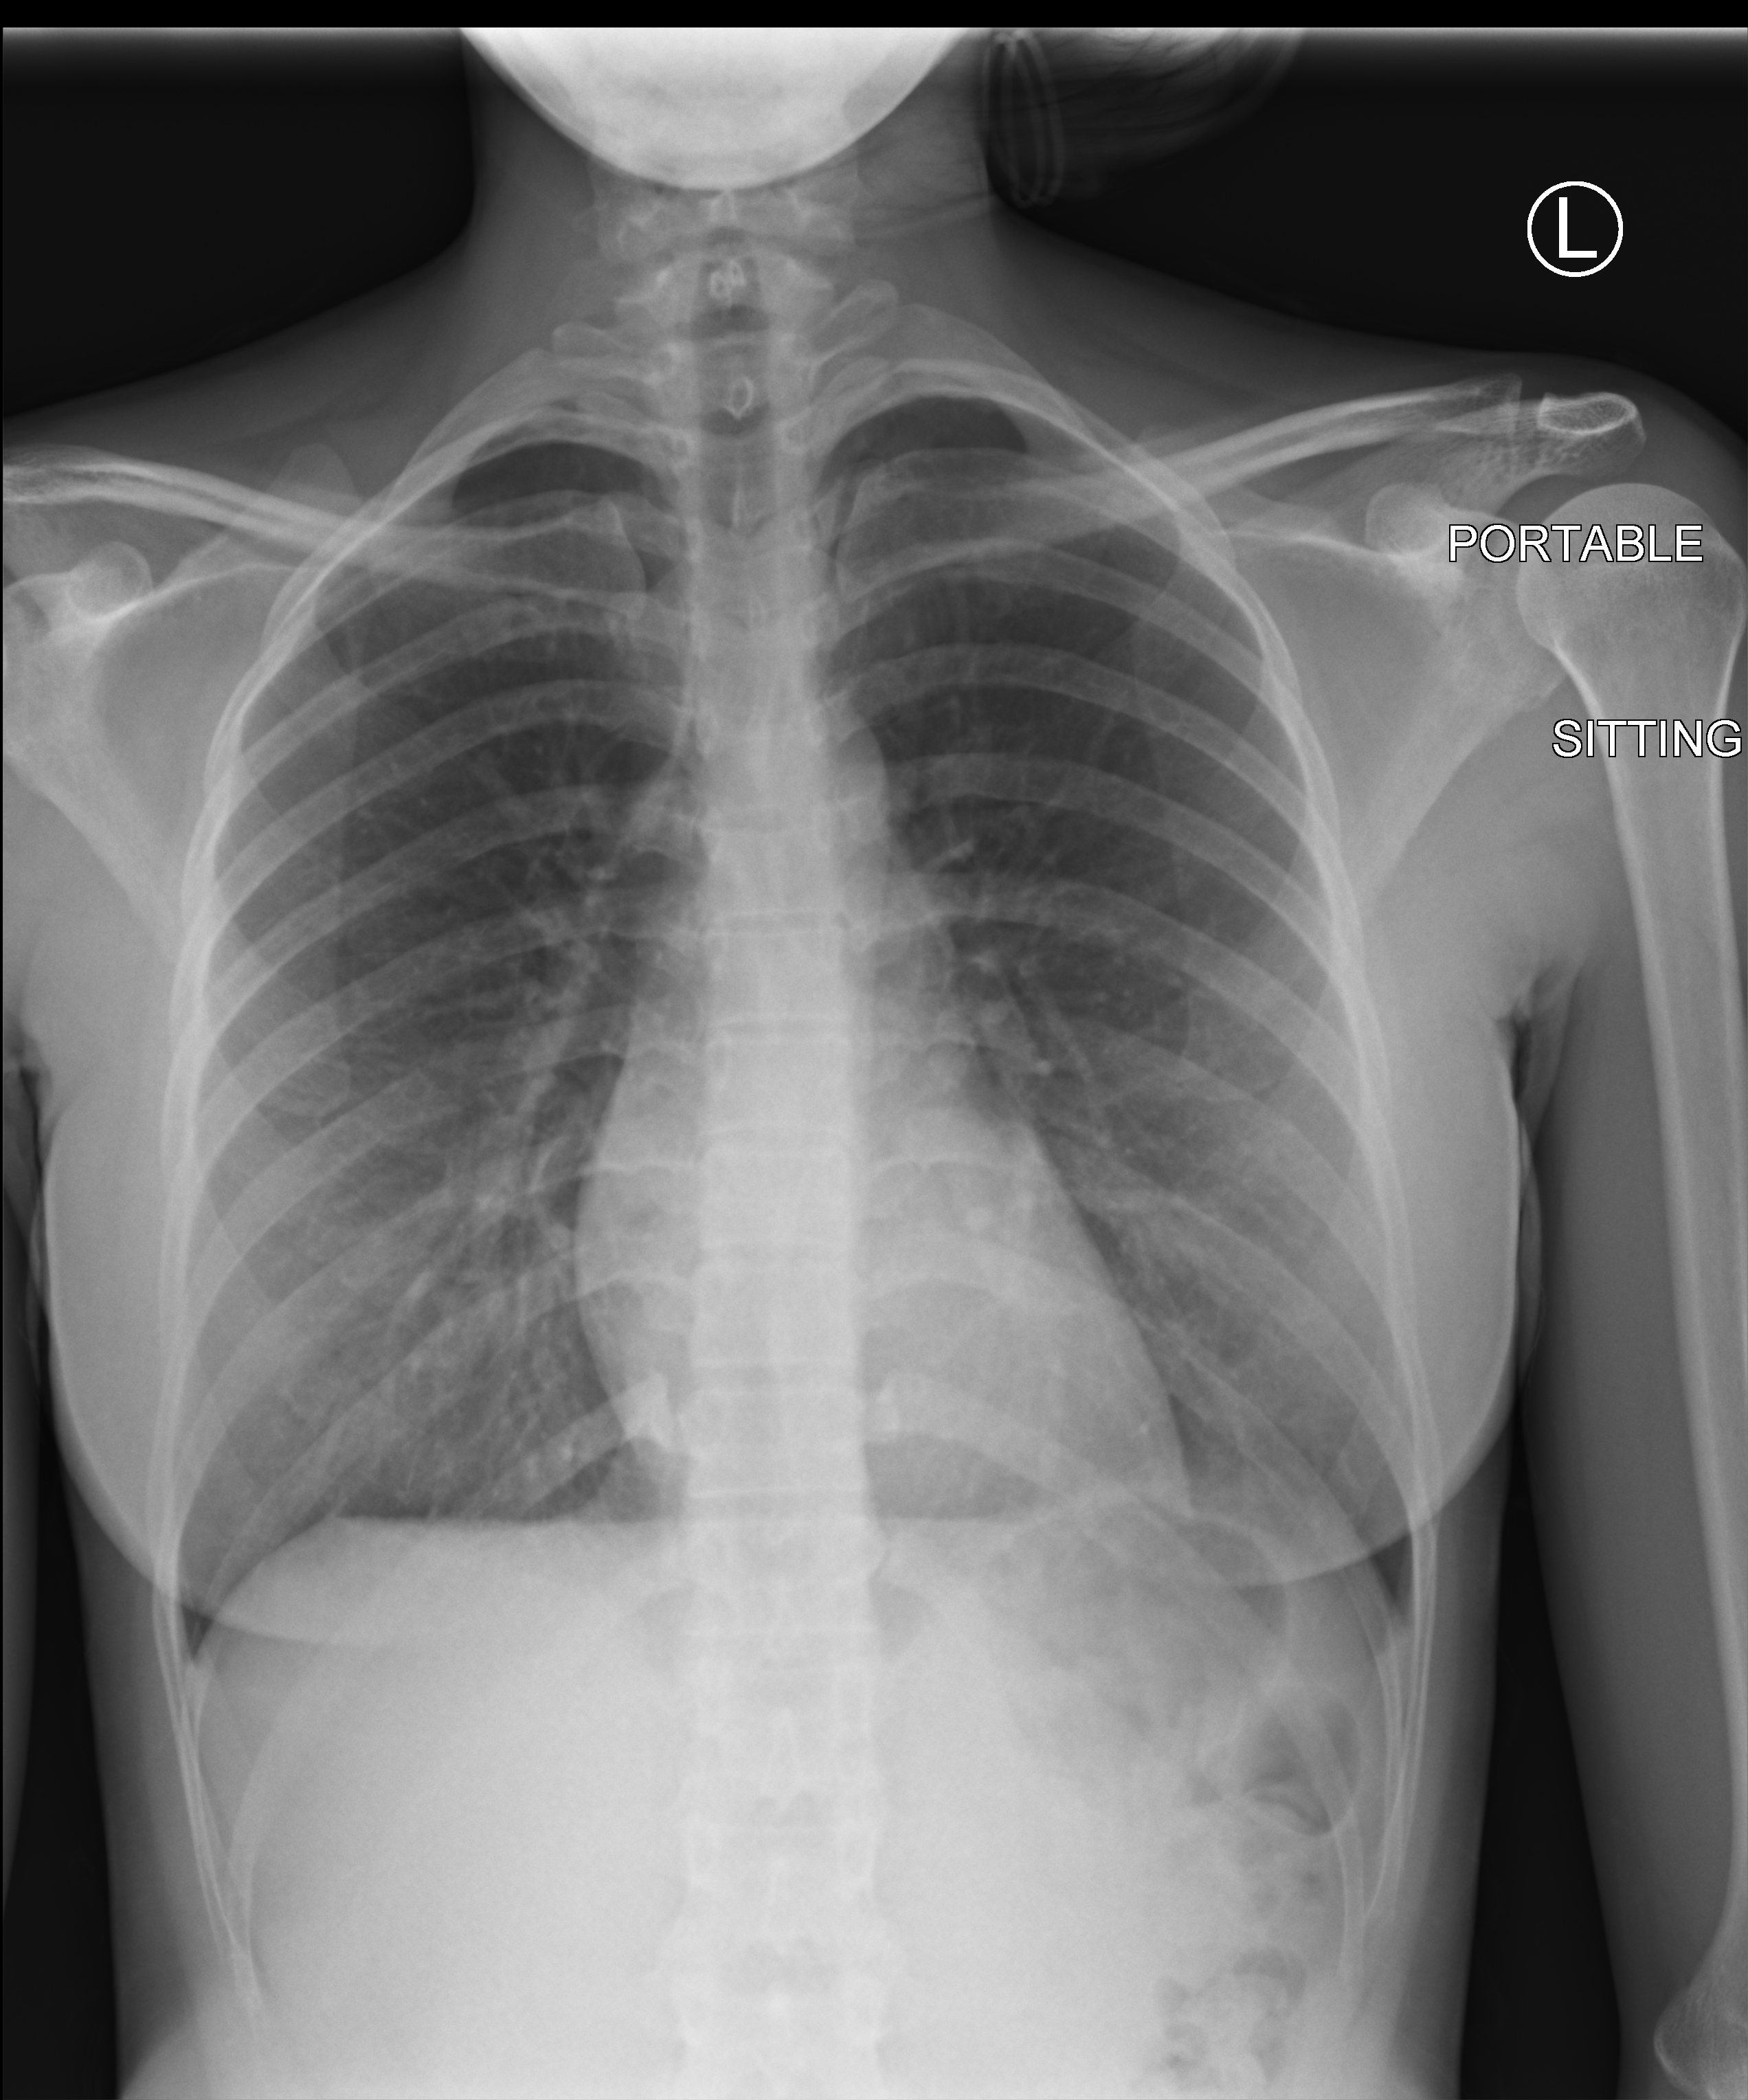
Bedside chest radiograph (computed radiography); anteroposterior (AP) projection. Patient hospitalised with COVID-19; female, aged 18–59 years.
Admission-level facts for this patient (not findings on this image; timing relative to this image not recorded): smoking status (admission record): current; length of hospital stay: 1 day.